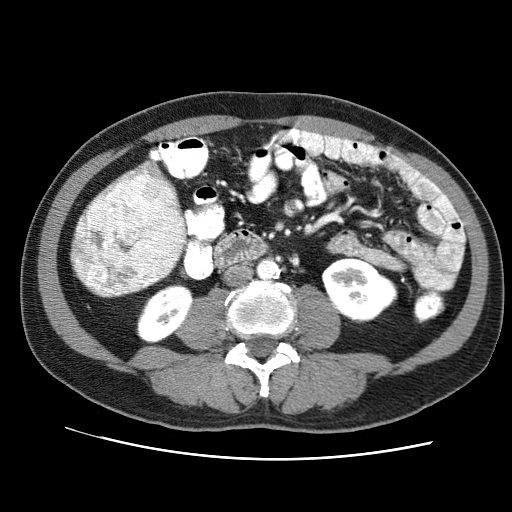
Contrast-enhanced abdominal CT (liver protocol), one axial slice. Slice 13 of 71 in the series (ordered by position). 120 kVp. Soft-tissue window (W 400 / L 40 HU). 2.5 mm slice thickness. 512 × 512 image matrix, field of view 360 × 360 mm. Case-level facts recorded for this patient, not image findings: diagnosis: hepatocellular carcinoma (patient treated with transarterial chemoembolisation; whether this scan precedes or follows treatment is not stated here); TNM stage (as recorded): Stage-II; Child-Pugh class: A; tumour nodularity: multinodular; tumour size: 4.6 cm.
Annotated regions visible in this slice (semi-automatic segmentation, software-assisted and operator-edited):
- liver parenchyma outside the tumour (the mass and vessels are separate outlines, so this box may not span the whole liver): box from (x=70, y=170) to (x=187, y=296) px
- mass: (x=69, y=178)–(x=186, y=297)
- liver vessels: (x=135, y=171)–(x=163, y=184)